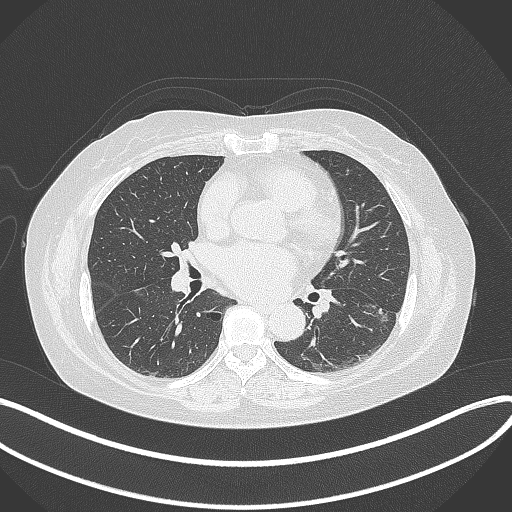
Chest CT, one axial slice; position 178 of 373 along the scan axis; reconstruction kernel B70f; 120 kVp; lung window (W 1500 / L -600 HU); 1 mm slice thickness; 512 × 512 image matrix, field of view 400 × 400 mm. Patient: female, 67 years. From the clinical record (not read from this slice): clinical TNM (as recorded): T1c N0 M0; histopathological grade: G2.
Outlined on this slice (rectangle marked by the reading radiologist):
- lung tumour (recorded histology: adenocarcinoma): bounding box [x1, y1, x2, y2] px = [367, 296, 393, 325]